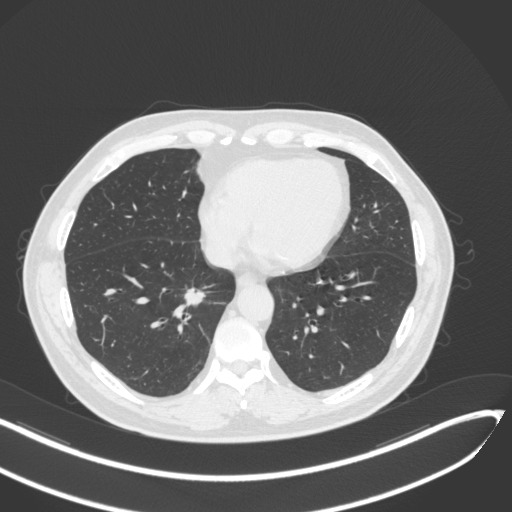
Chest CT, one axial slice. Slice 131 of 429 in the series (ordered by position). Reconstruction kernel B31f. Lung window (W 1500 / L -600 HU). 1 mm slice thickness. 512 × 512 image matrix, field of view 400 × 400 mm. Male patient, age 62 years. Case-level facts recorded for this patient, not image findings: clinical TNM (as recorded): T1b N0 M0; histopathological grade: G2.
Structures marked on this image (bounding box drawn by a radiologist):
- lung tumour (recorded histology: adenocarcinoma): bounding box [x1, y1, x2, y2] px = [185, 285, 216, 312]